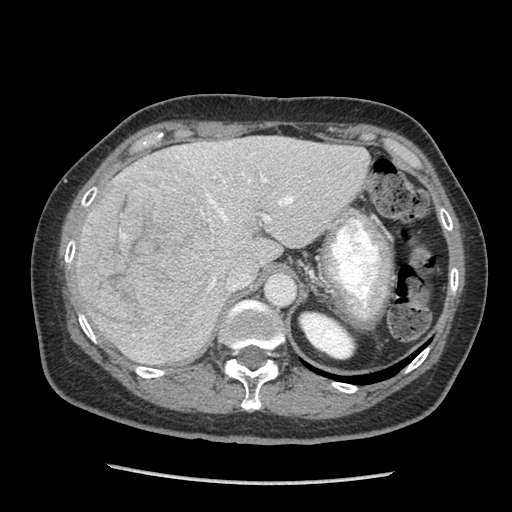
Contrast-enhanced abdominal CT (liver protocol), one axial slice; 140 kVp; soft-tissue window (W 400 / L 40 HU); 512 × 512 image matrix. Case-level facts recorded for this patient, not image findings: diagnosis: hepatocellular carcinoma (patient treated with transarterial chemoembolisation; whether this scan precedes or follows treatment is not stated here); TNM stage (as recorded): Stage-I; Child-Pugh class: A; tumour differentiation: moderately differentiated; tumour nodularity: uninodular.
Structures marked on this image (semi-automatic segmentation, software-assisted and operator-edited):
- abdominal aorta: box from (x=267, y=275) to (x=295, y=304) px
- liver parenchyma outside the tumour (the mass and vessels are separate outlines, so this box may not span the whole liver): (x=74, y=136)–(x=368, y=364)
- mass: (x=78, y=177)–(x=219, y=339)
- liver vessels: (x=175, y=143)–(x=294, y=288)